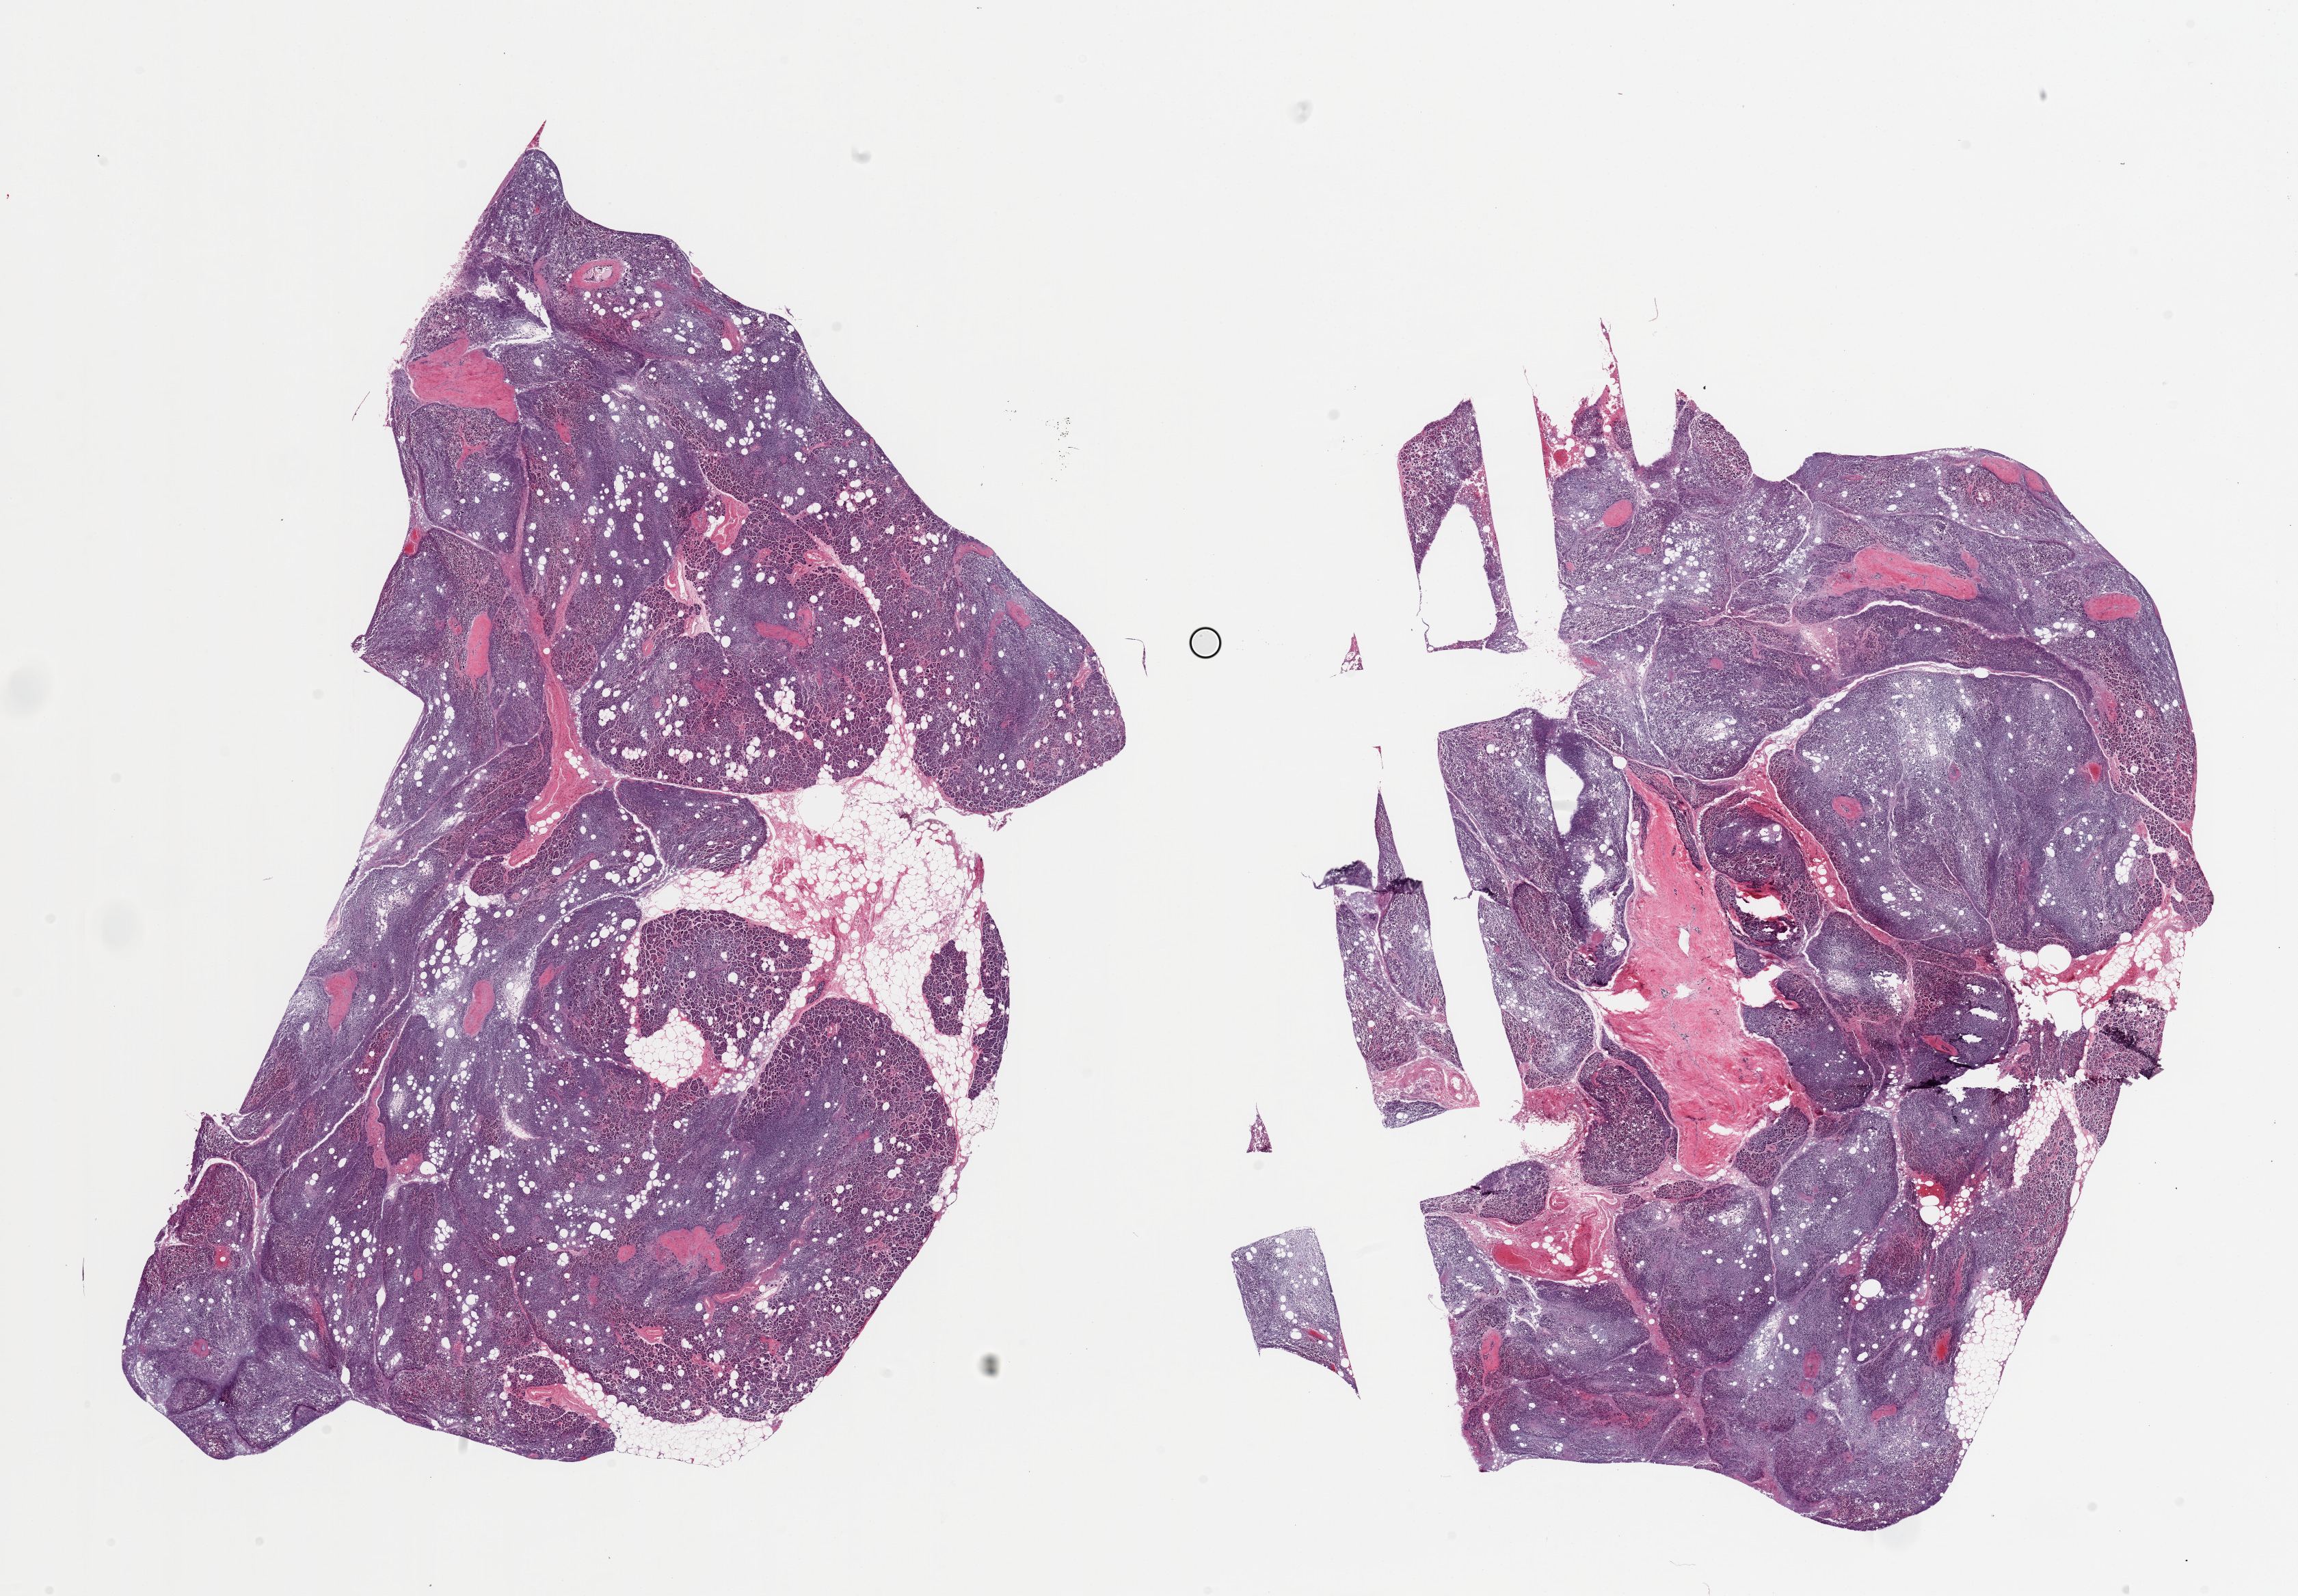
Whole-slide image, H&E stain — shown as a low-resolution overview of the whole scanned area (about 26.6 x 18.5 mm, slide scanned at 20x), PAXgene-fixed paraffin-embedded (PFPE) section, section of pancreas (target tissue), tissue donor sample. Male donor.
Review note (as recorded): 2 pieces, advanced saponification/autolysis.